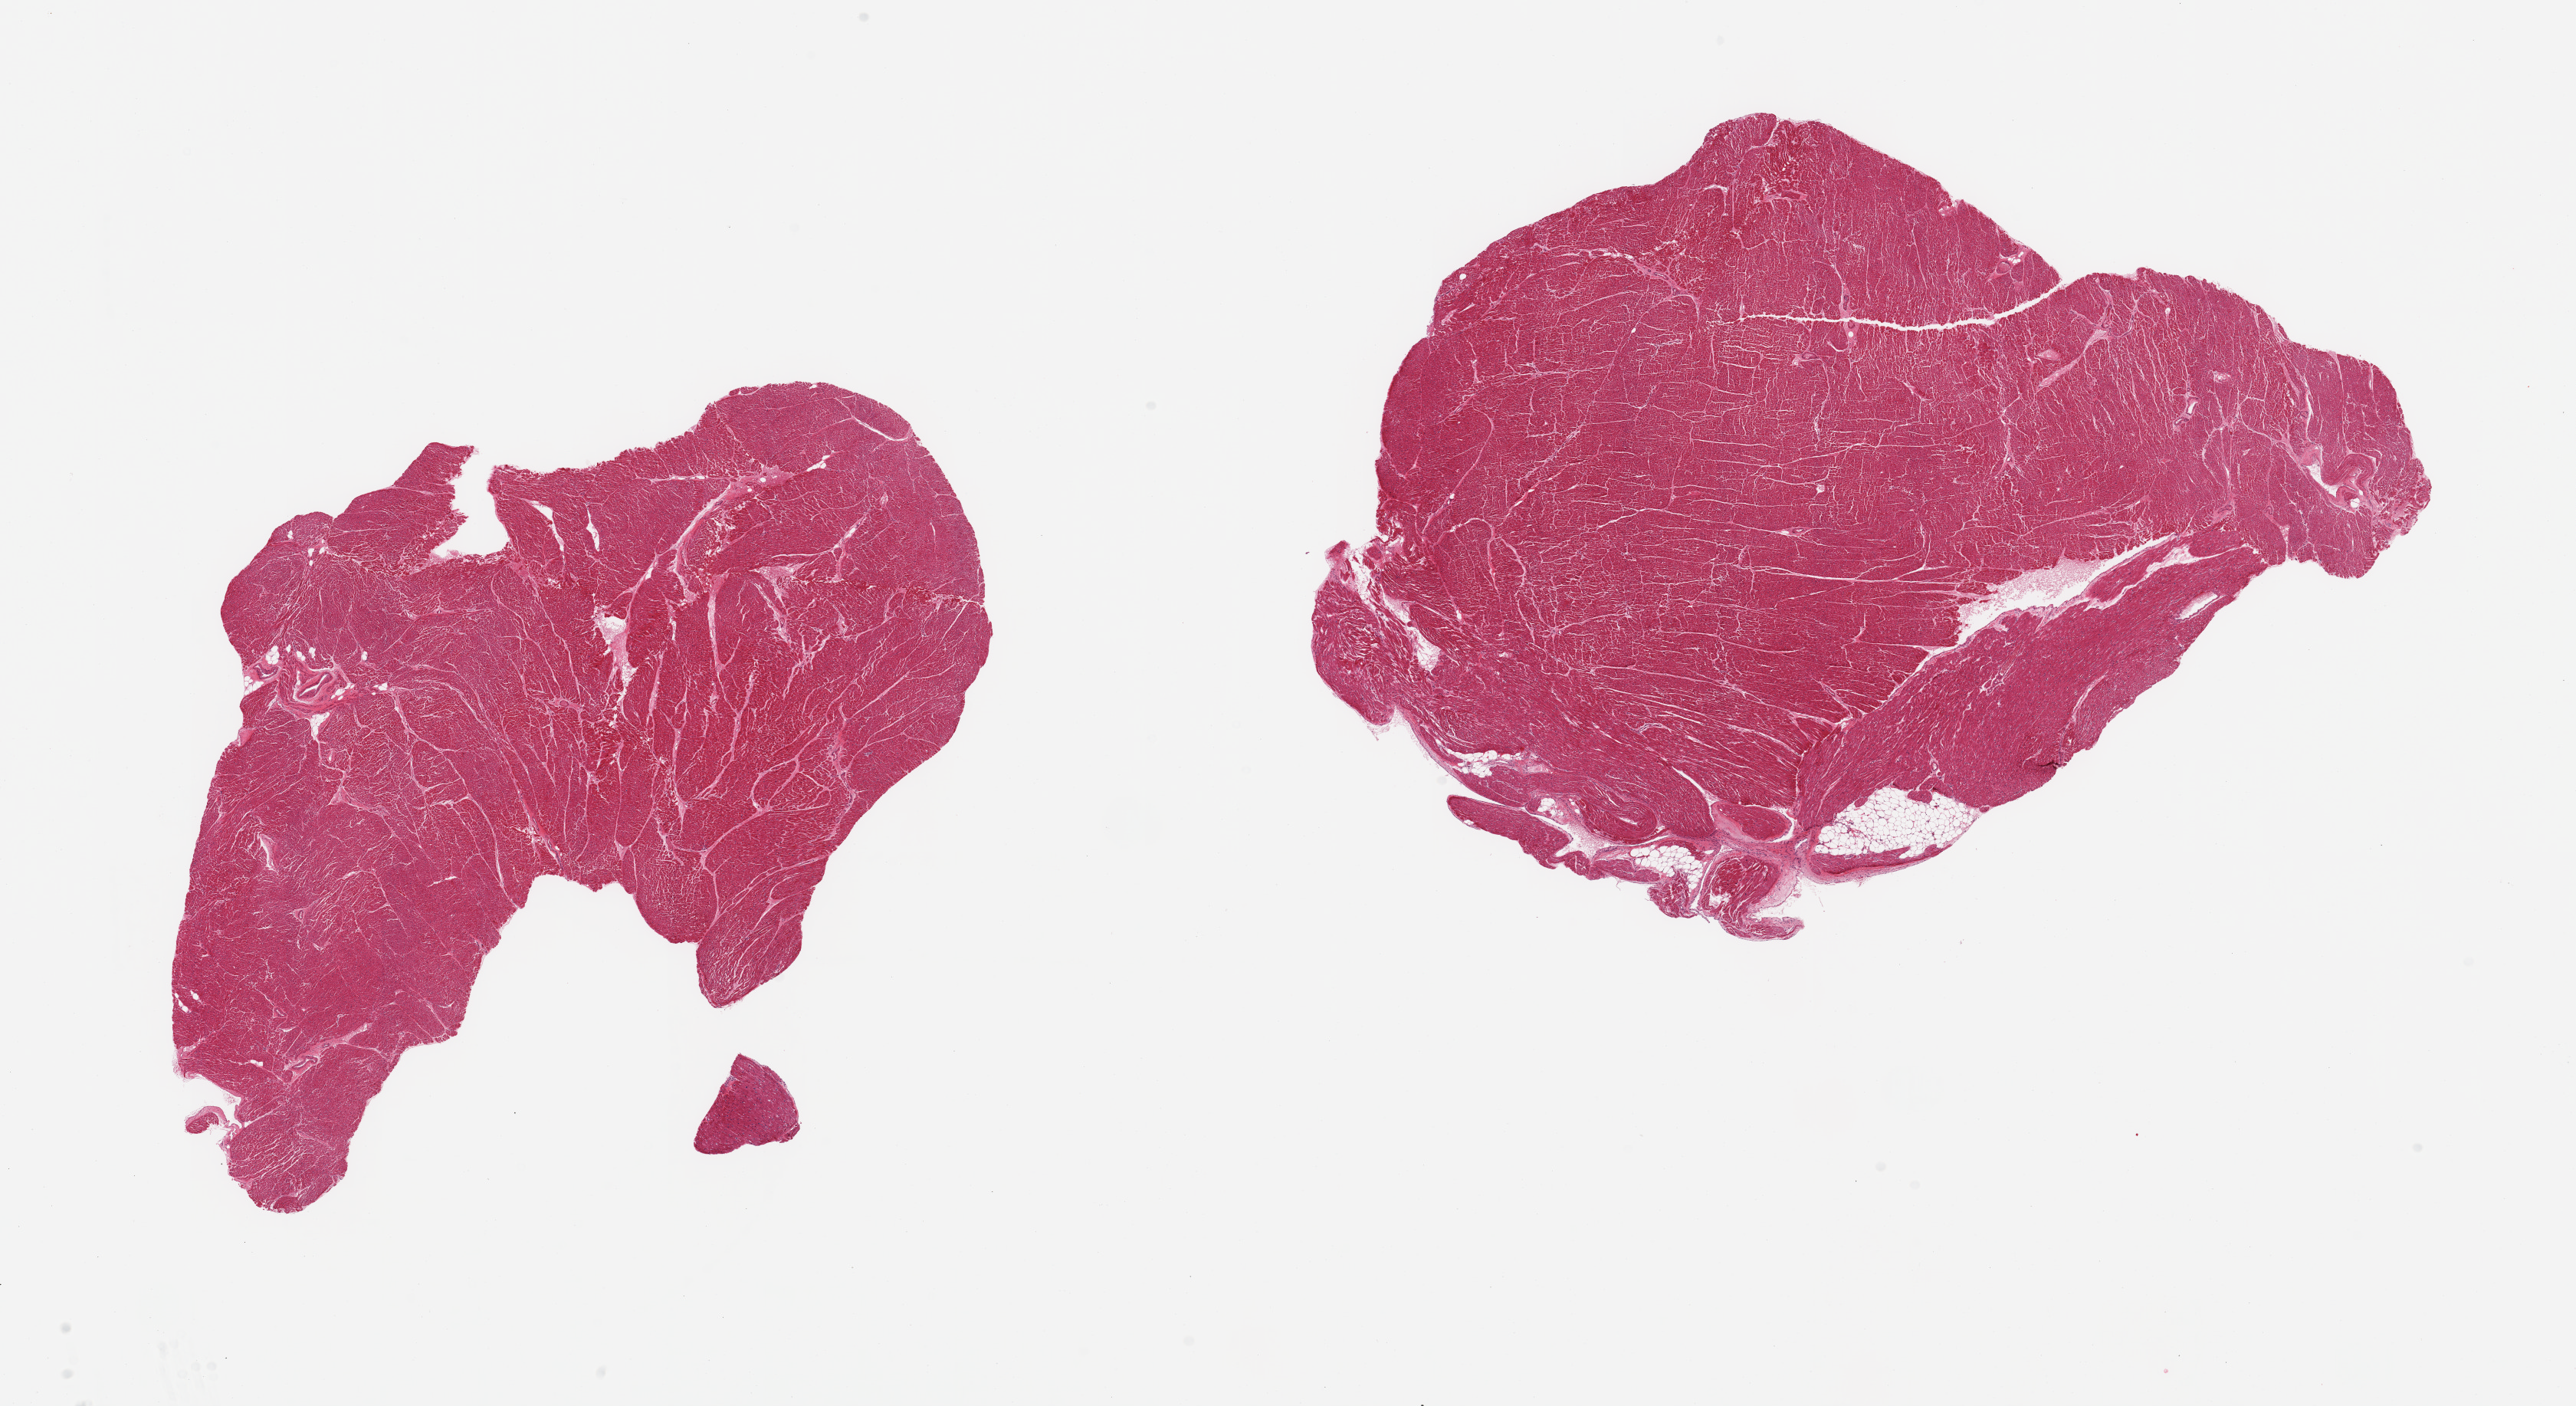
Hematoxylin and eosin (H&E) whole-slide image, low-resolution overview of the scanned area, about 26.6 x 14.5 mm (from a 20x scan); PAXgene-fixed paraffin-embedded (PFPE) section; section of heart (target tissue); tissue donor sample. Donor: male.
• reviewer comment on this tissue sample: 2 pieces, minimal interstitial fibrosis/chronic ischemic changes